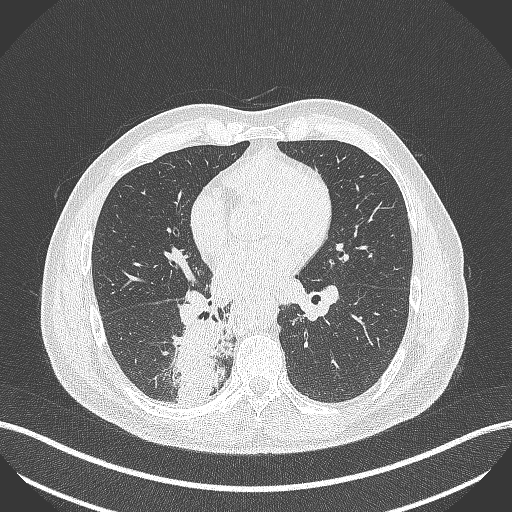
Chest CT, one axial slice; slice 223 of 451 in the series (ordered by position); reconstruction kernel B70f; lung window (W 1500 / L -600 HU); 1 mm slice thickness; 512 × 512 image matrix, field of view 400 × 400 mm. Male patient, age 61 years. Case-level facts recorded for this patient, not image findings: clinical TNM (as recorded): T1 N0 M0; histopathological grade: G3.
Annotated regions visible in this slice (rectangle marked by the reading radiologist):
- lung tumour (recorded histology: small cell carcinoma): bounding box <169,320,231,409> (left, top, right, bottom; pixels)